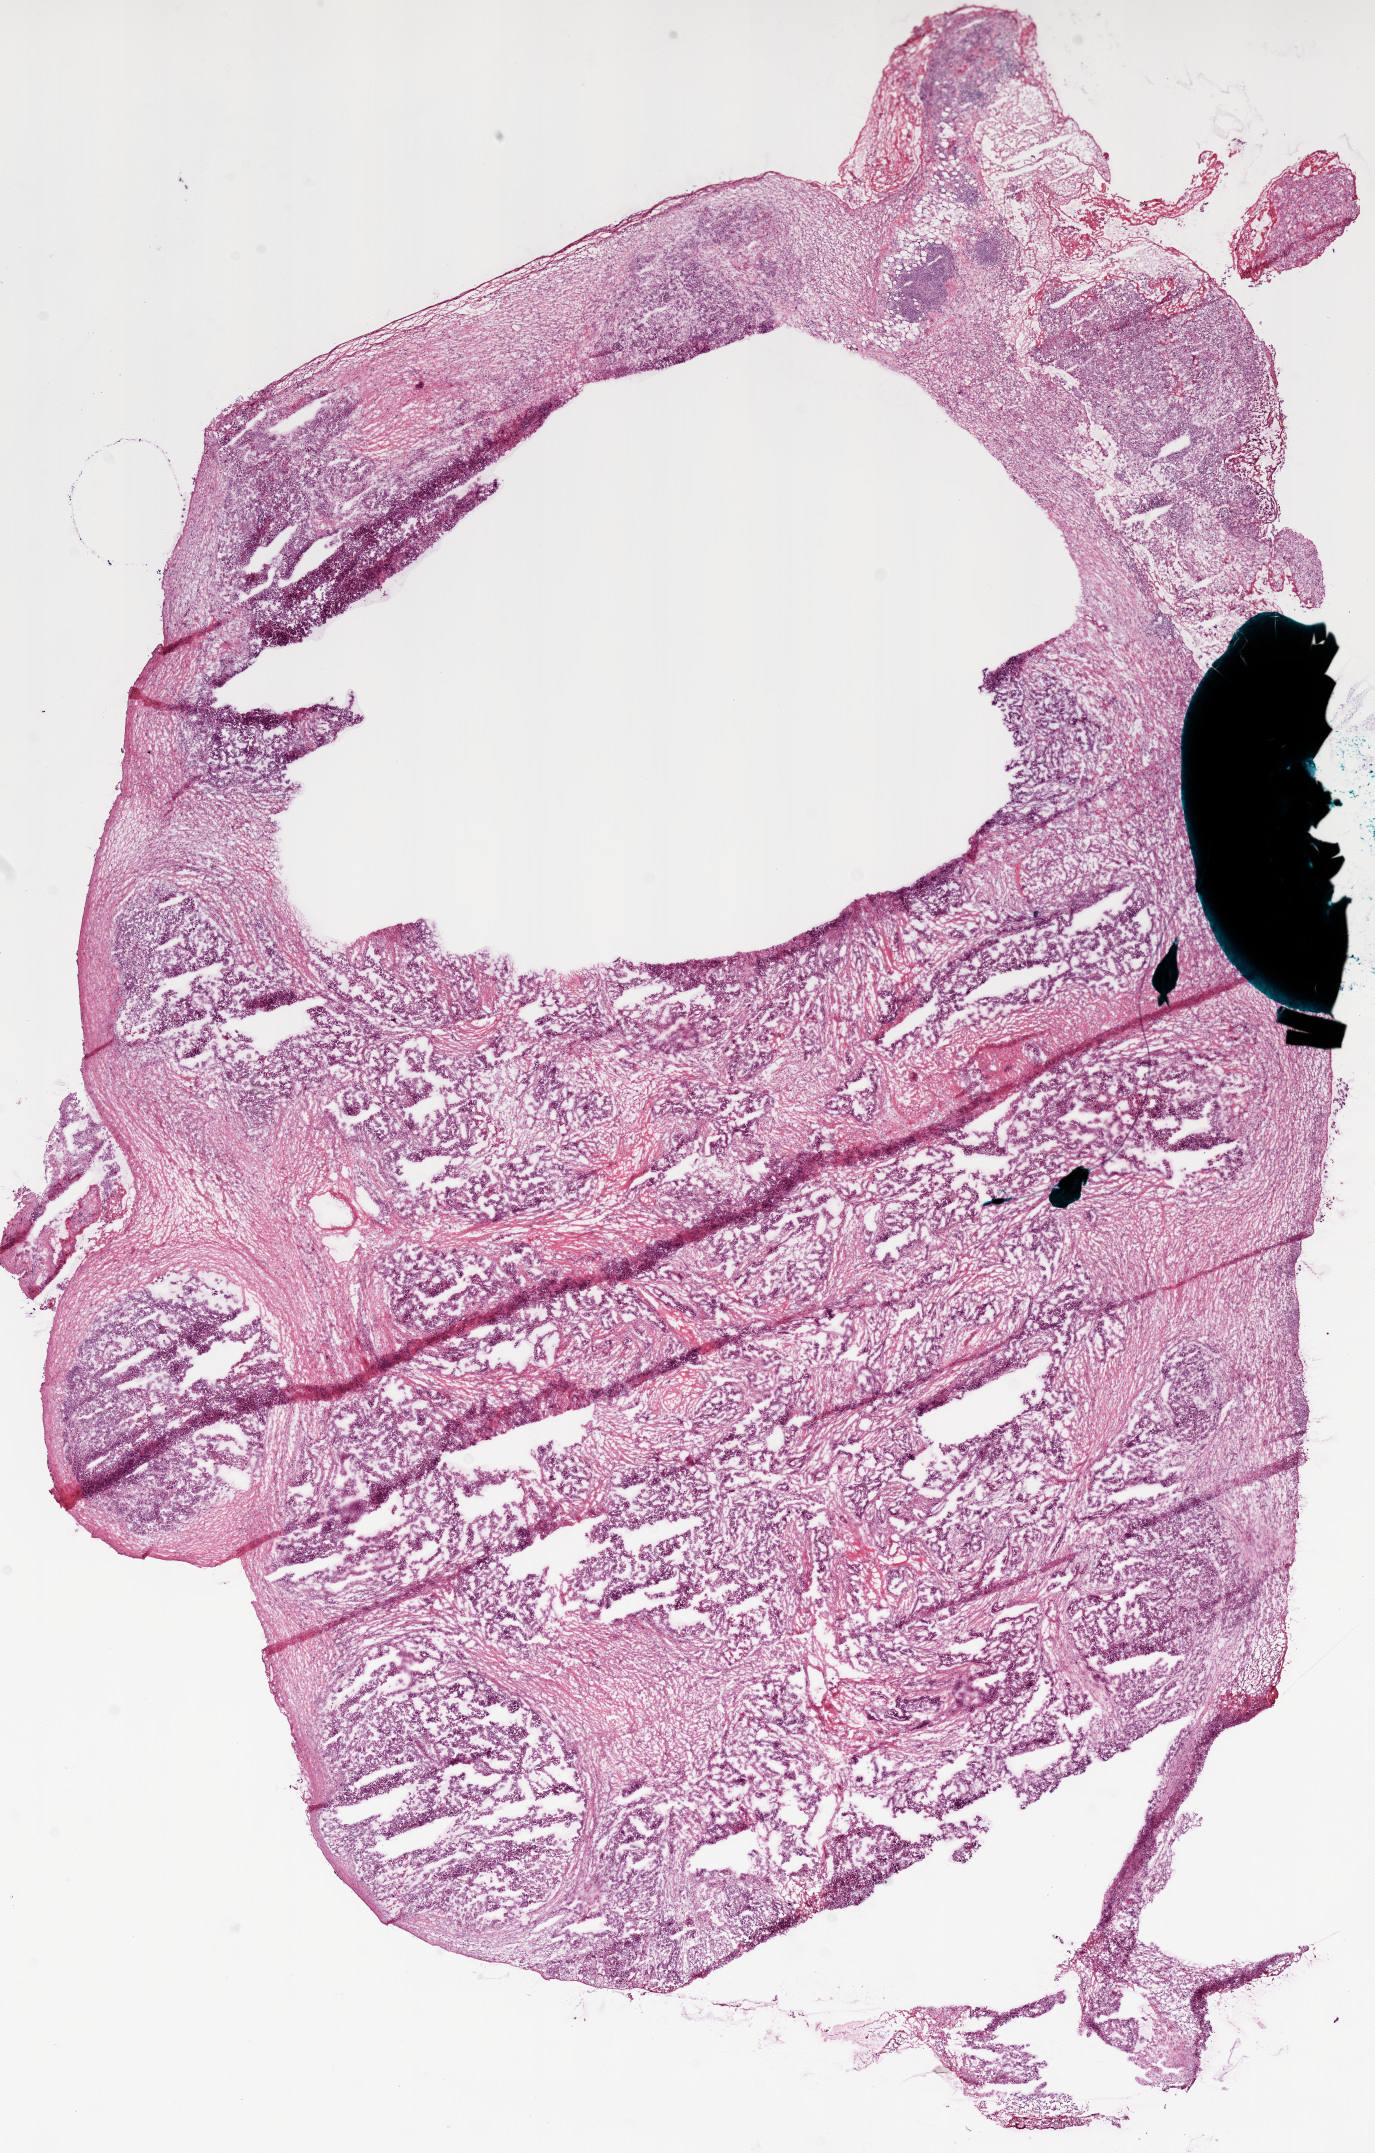
Whole-slide histology image, Hematoxylin and eosin (H&E) stained — a low-resolution overview of the entire scanned area, about 11.0 x 17.3 mm, frozen section, sample: primary tumour, ovary. Patient: female, age at initial diagnosis 59 years. Pathologist review of this section (percent, as recorded): tumour cells 79%, tumour nuclei 80%.
Histologic diagnosis: Serous cystadenocarcinoma, NOS.